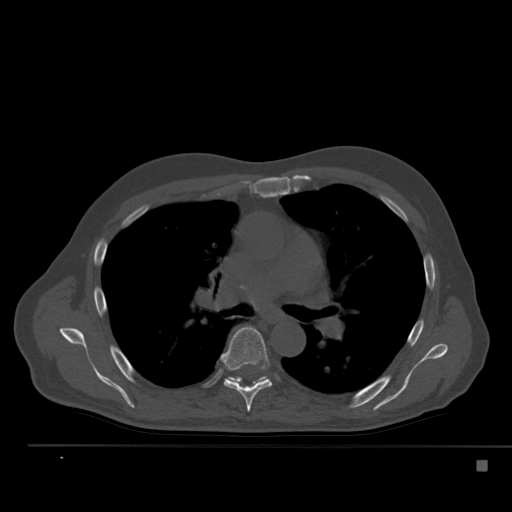
CT including the spine, one axial slice; slice 344 of 517 in the series (ordered by position); reconstruction kernel Br40s; 120 kVp; bone window (W 1800 / L 400 HU); 512 × 512 image matrix, field of view 408 × 408 mm. Male patient, age 70 years. Case-level facts recorded for this patient, not image findings: primary cancer: renal; vertebrae with lytic lesions (as recorded): T4, T6, T10, T12, L3, L4, L5.
Structures marked on this image (semi-automatically segmented with operator editing):
- T6 vertebra: bounding box [x1, y1, x2, y2] px = [220, 326, 272, 412]
- T7 vertebra: [226, 376, 268, 383]